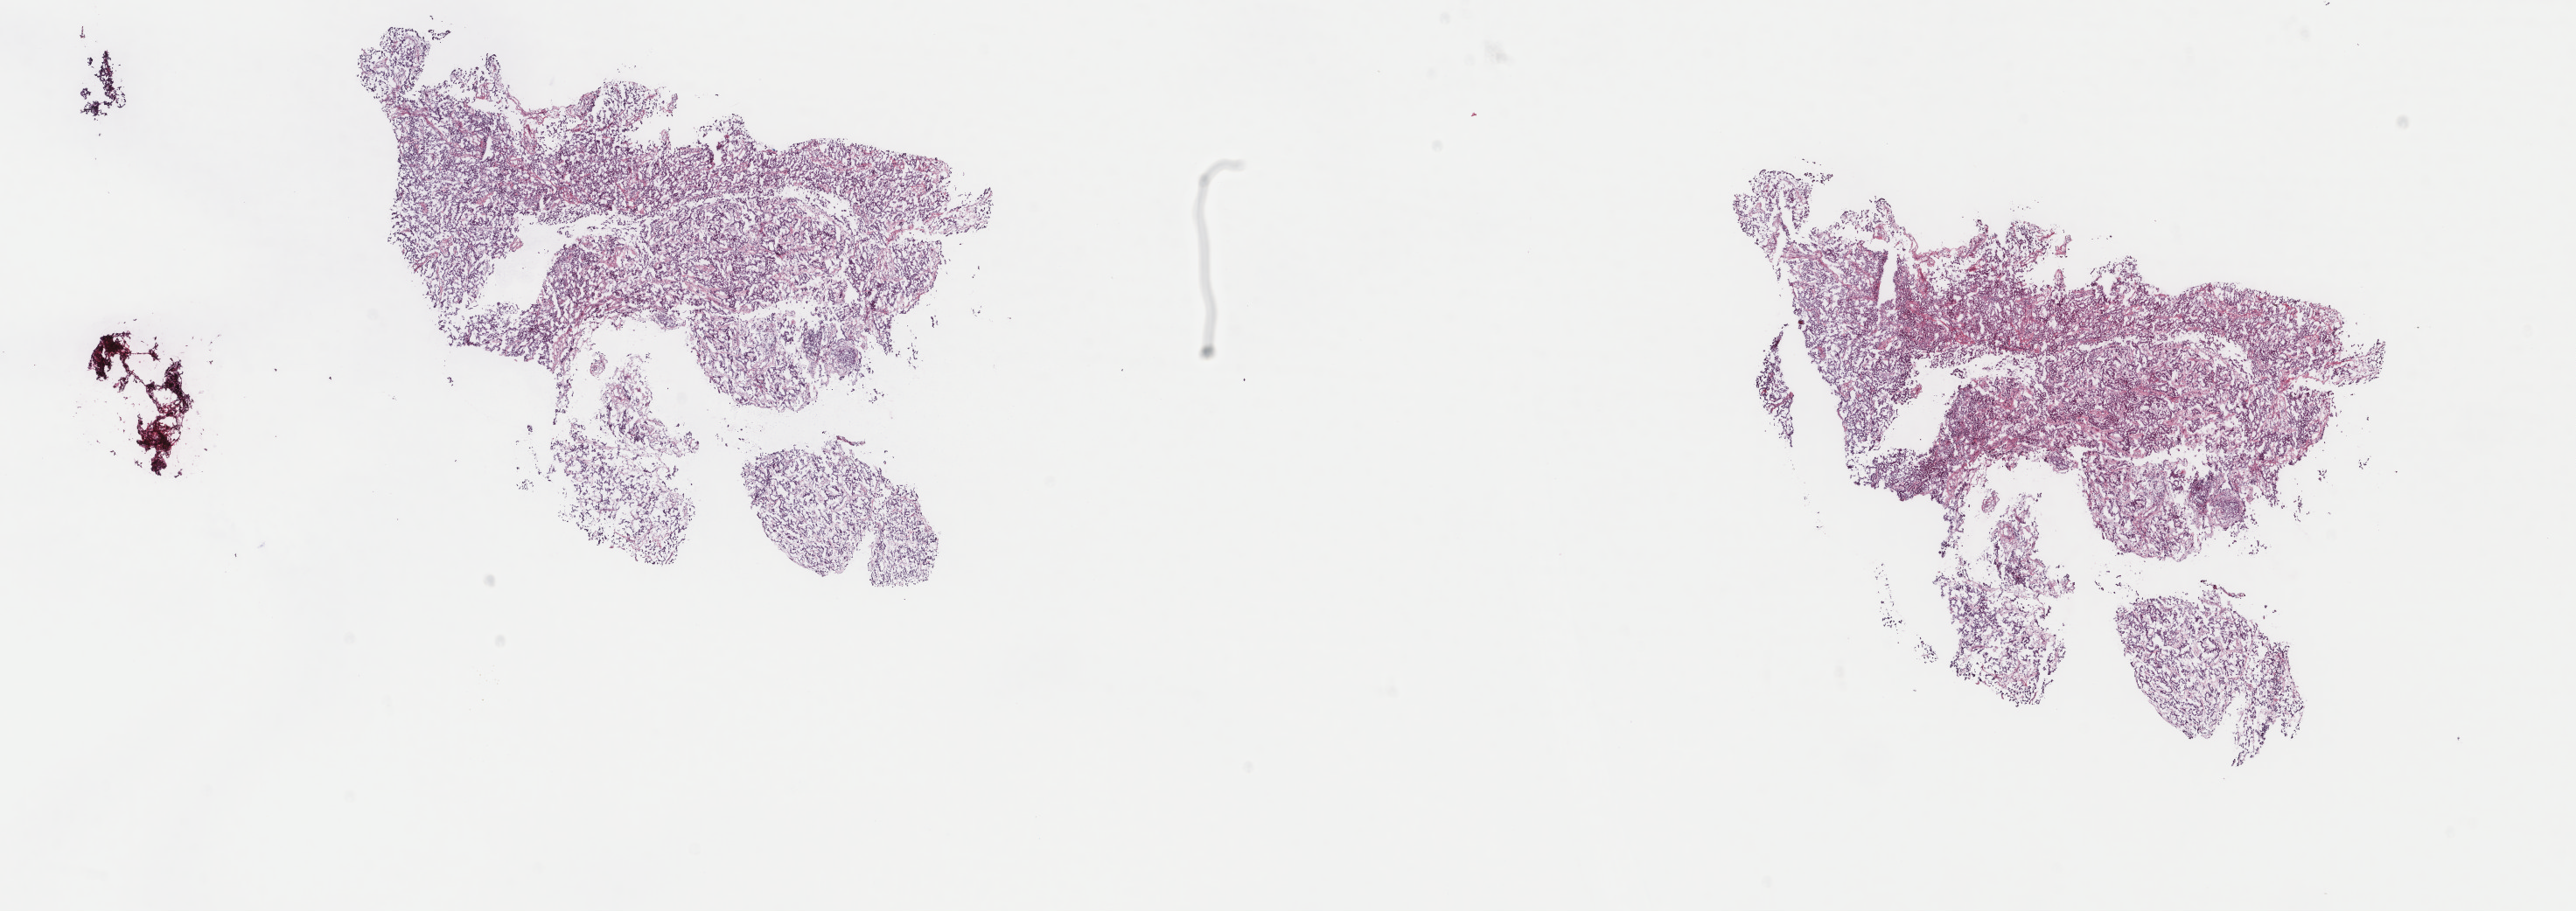
Hematoxylin and eosin (H&E) stained whole-slide image, a low-resolution overview of the entire scanned area, about 23.4 x 8.3 mm (slide scanned at 40x), frozen section from the top of the tissue portion, mesothelium, primary tumour sample. Male patient; age at initial diagnosis 58 years. Pathologist review of this section (percent, as recorded): tumour cells 100%, tumour nuclei 80%, normal cells 0%, stromal cells 0%, necrosis 0%. Infiltration values recorded for this section: lymphocyte infiltration 2%, monocyte infiltration 0%, neutrophil infiltration 0%.
Pathologic diagnosis: Epithelioid mesothelioma, malignant. AJCC pathologic stage: II (6th edition).